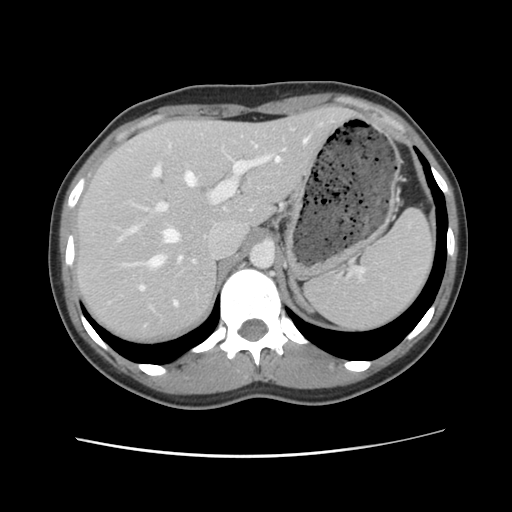
Contrast-enhanced abdominal CT, one axial slice. 120 kVp. Soft-tissue window (W 400 / L 40 HU). 512 × 512 image matrix, field of view 339 × 339 mm. Female patient, age 33 years. From the clinical record (not read from this slice): diagnosis: colorectal cancer liver metastases, imaged before liver resection; multiple liver metastases: yes; largest metastasis: 4.5 cm; disease in both lobes: yes.
Structures marked on this image (expert manual segmentation):
- hepatic veins: box from (x=149, y=138) to (x=309, y=306) px
- liver: (x=77, y=107)–(x=352, y=344)
- planned liver remnant (the part of the liver to remain after resection): (x=77, y=108)–(x=353, y=344)
- portal vein (with intrahepatic branches): (x=120, y=139)–(x=286, y=289)